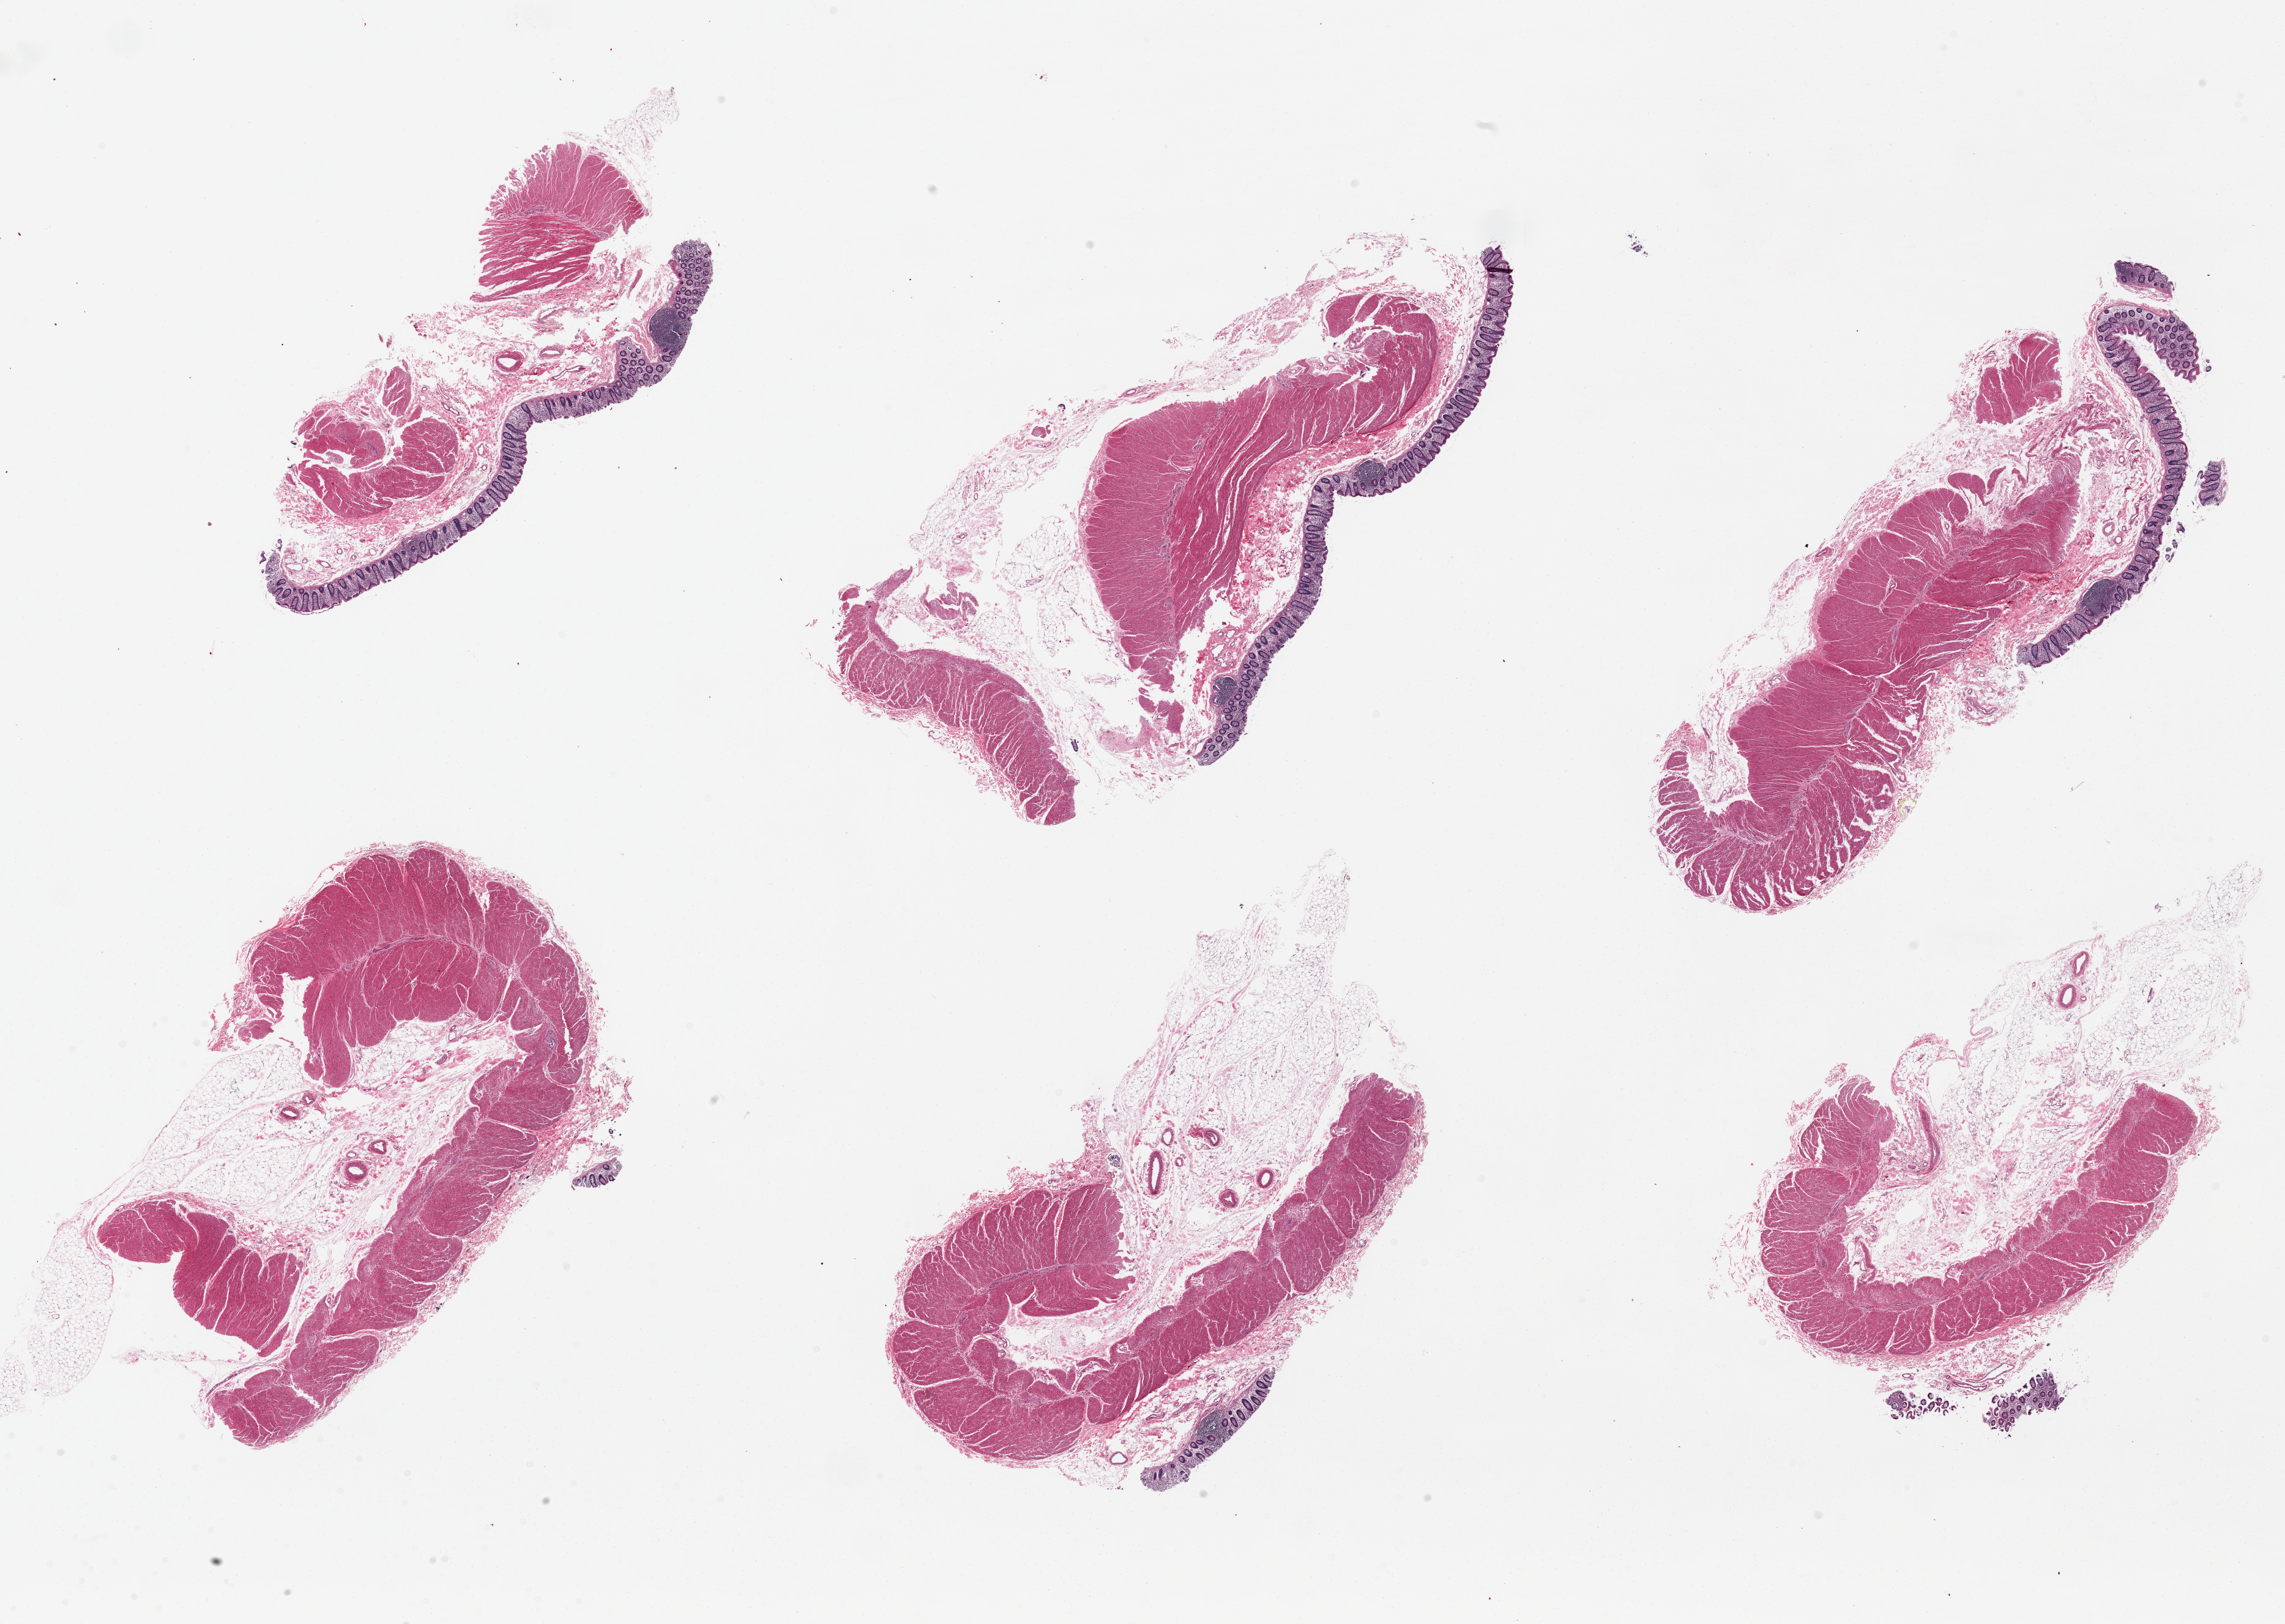
Haematoxylin and eosin whole-slide image, brightfield — whole scanned area (about 29.5 x 21.0 mm, from a 20x scan) shown as a low-resolution overview. PAXgene-fixed, paraffin-embedded tissue. Target tissue: sigmoid colon. Donor tissue sample. Female donor.
* reviewer comment on this tissue sample: 6 pieces. up to 10.5x5mm; All have mucosa, 3 with large amounts. TARGET is muscularis propria; discard mucosa